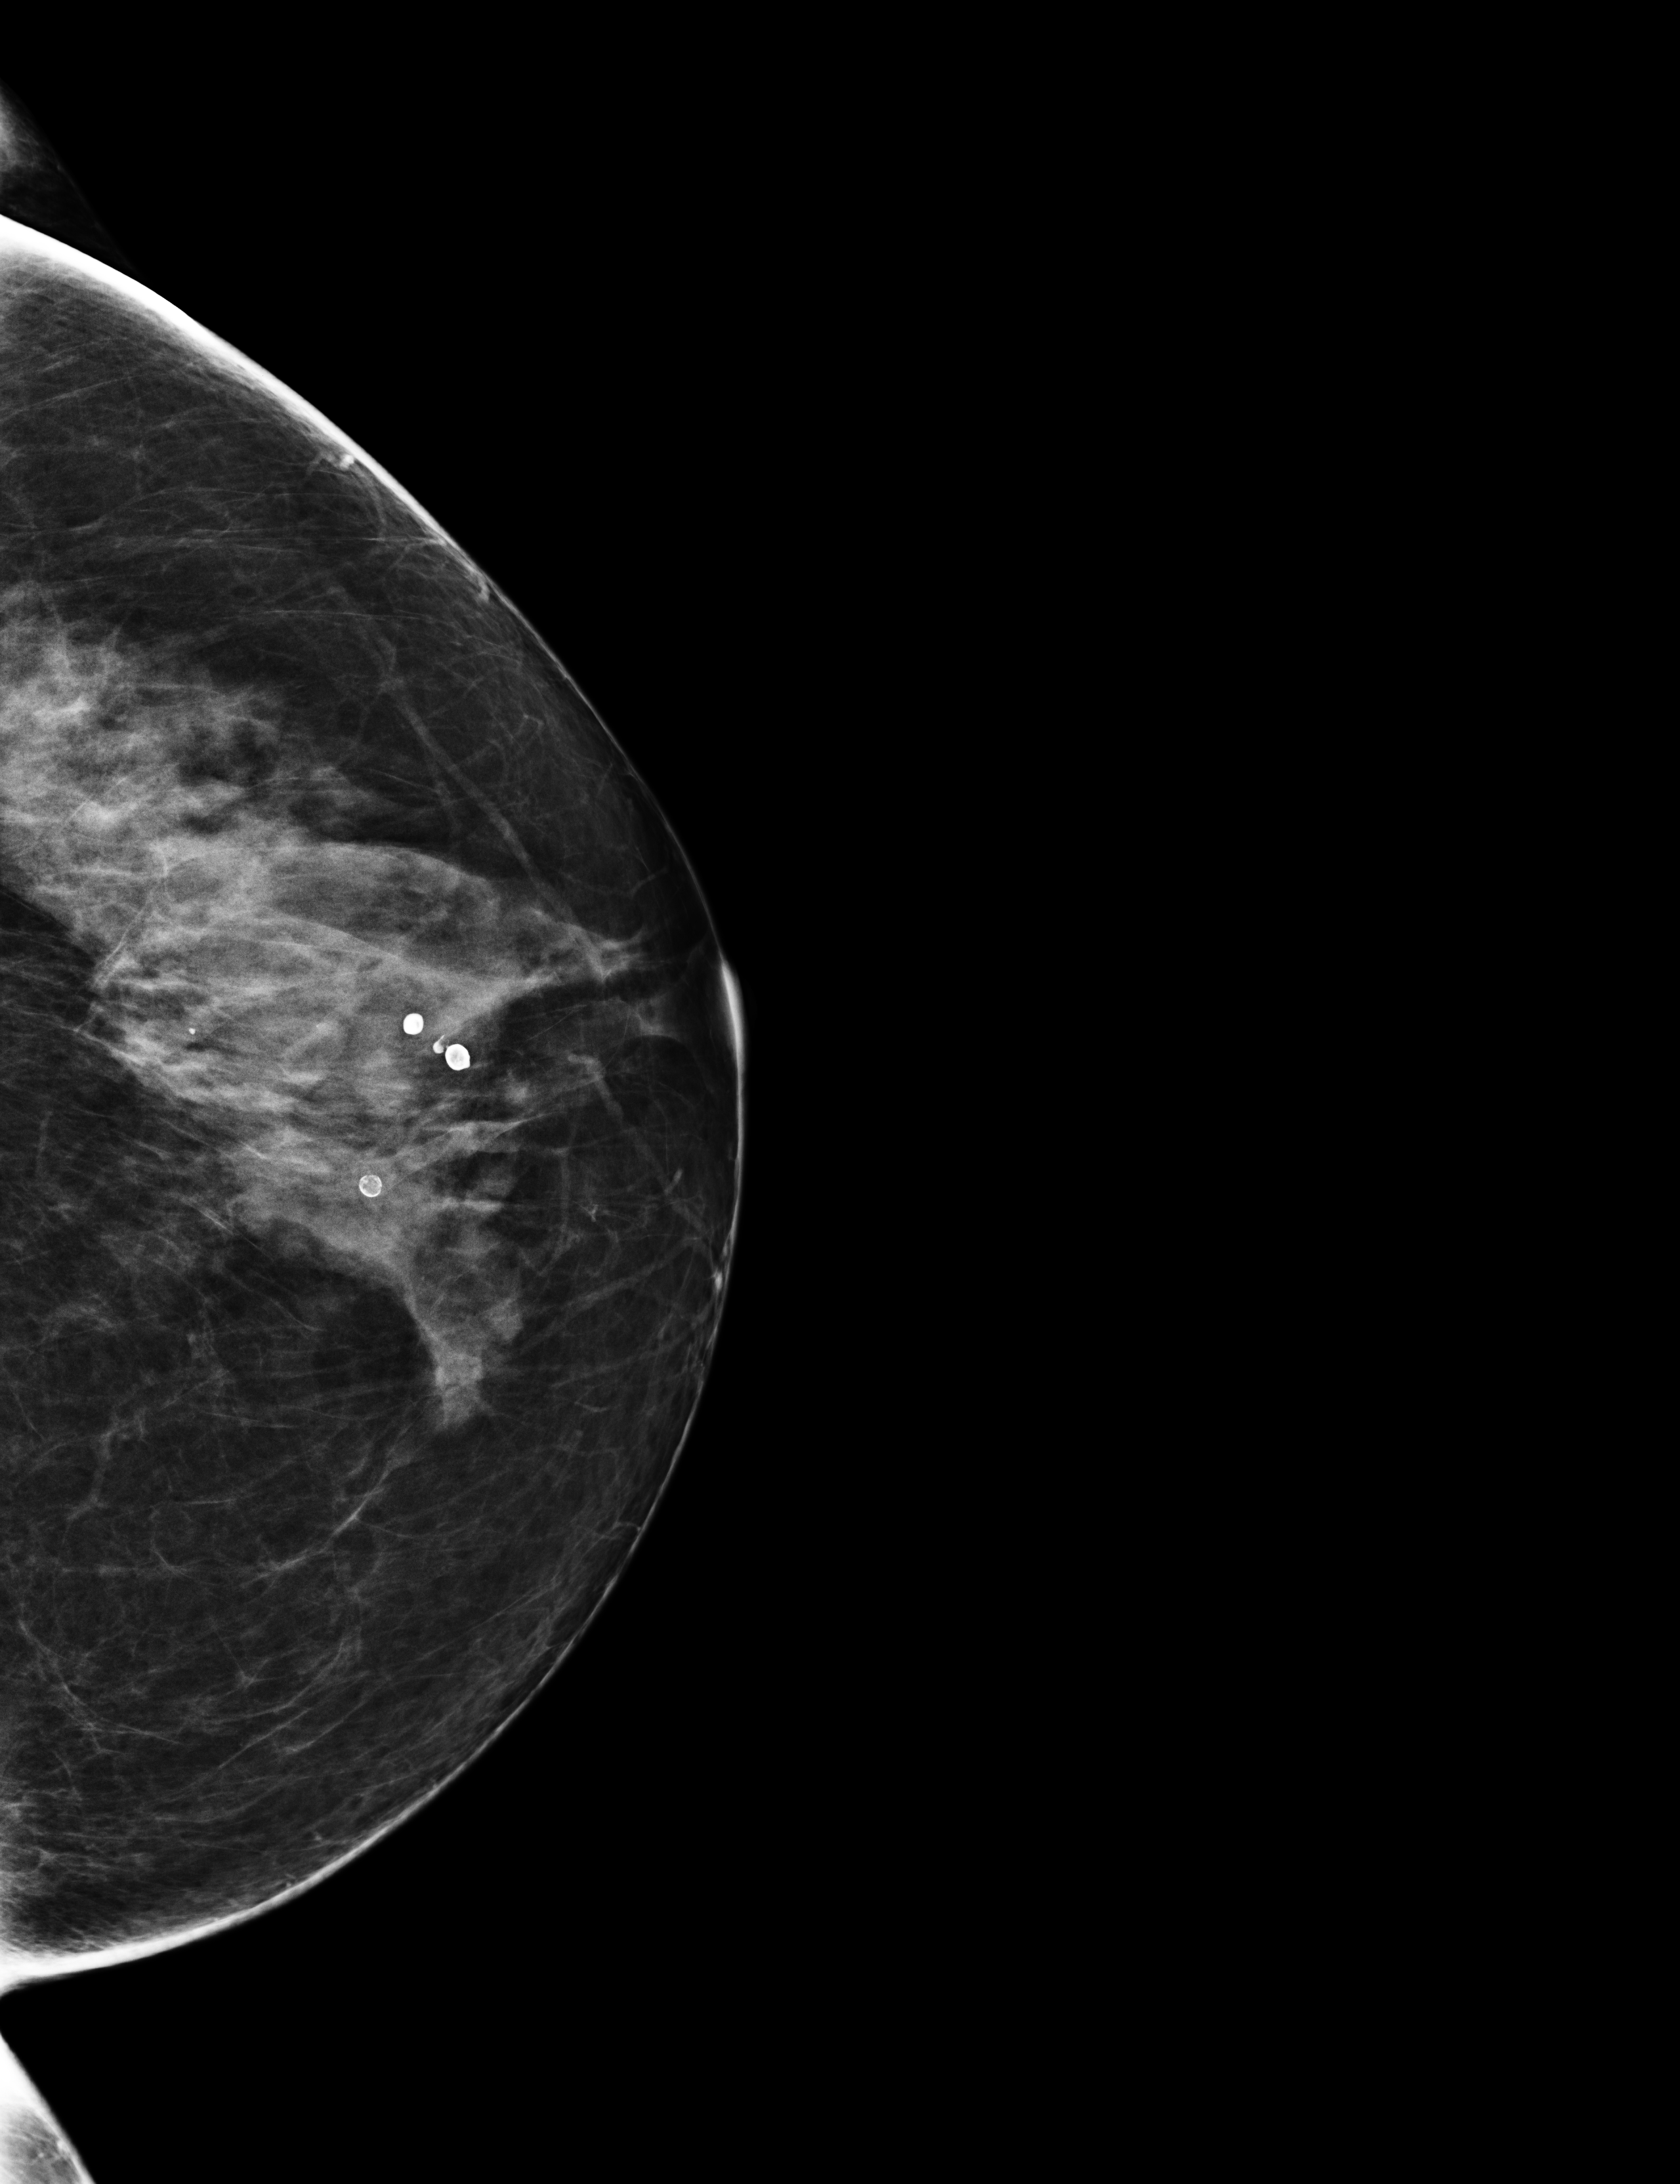
Full-field digital mammogram (FFDM), left breast, craniocaudal (CC) view, annual screening mammography examination, compressed breast thickness 69 mm. Female patient, age 67 years.
Final BI-RADS assessment for this screening round (tomosynthesis exam, both breasts): category 1.